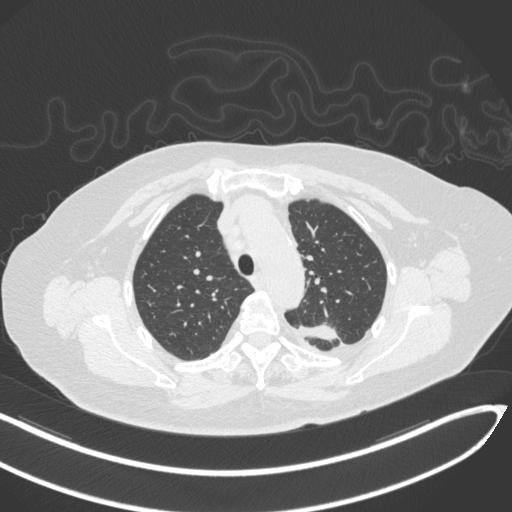
Chest CT, one axial slice. Position 242 of 270 along the scan axis. 120 kVp. Lung window (W 1500 / L -600 HU). 1 mm slice thickness. 512 × 512 image matrix, field of view 400 × 400 mm. Female patient, age 76 years. Case-level facts recorded for this patient, not image findings: clinical TNM (as recorded): T1c N0 M0.
Outlined on this slice (rectangle marked by the reading radiologist):
- lung tumour (recorded histology: adenocarcinoma): bounding box (x1, y1, x2, y2) in pixels: (299, 311, 340, 344)